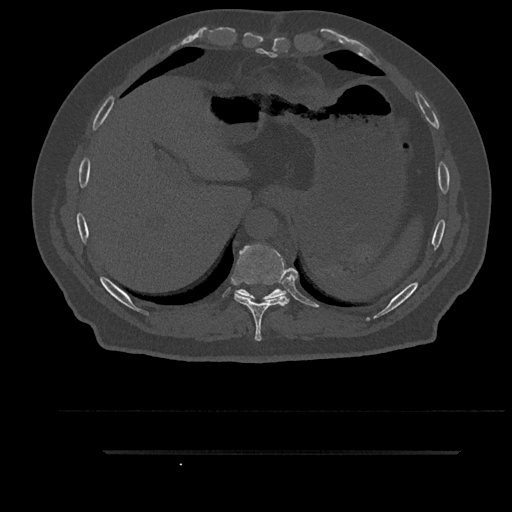
CT including the spine, one axial slice. Position 404 of 797 along the scan axis. 120 kVp. Bone window (W 1800 / L 400 HU). 0.5 mm slice thickness. 512 × 512 image matrix, field of view 432 × 432 mm. Patient: male, 63 years. From the clinical record (not read from this slice): primary cancer: renal; vertebrae with lytic lesions (as recorded): T8.
Structures marked on this image (semi-automatically segmented with operator editing):
- T10 vertebra: bounding box <235,288,287,300> (left, top, right, bottom; pixels)
- T9 vertebra: <234,244,289,341>